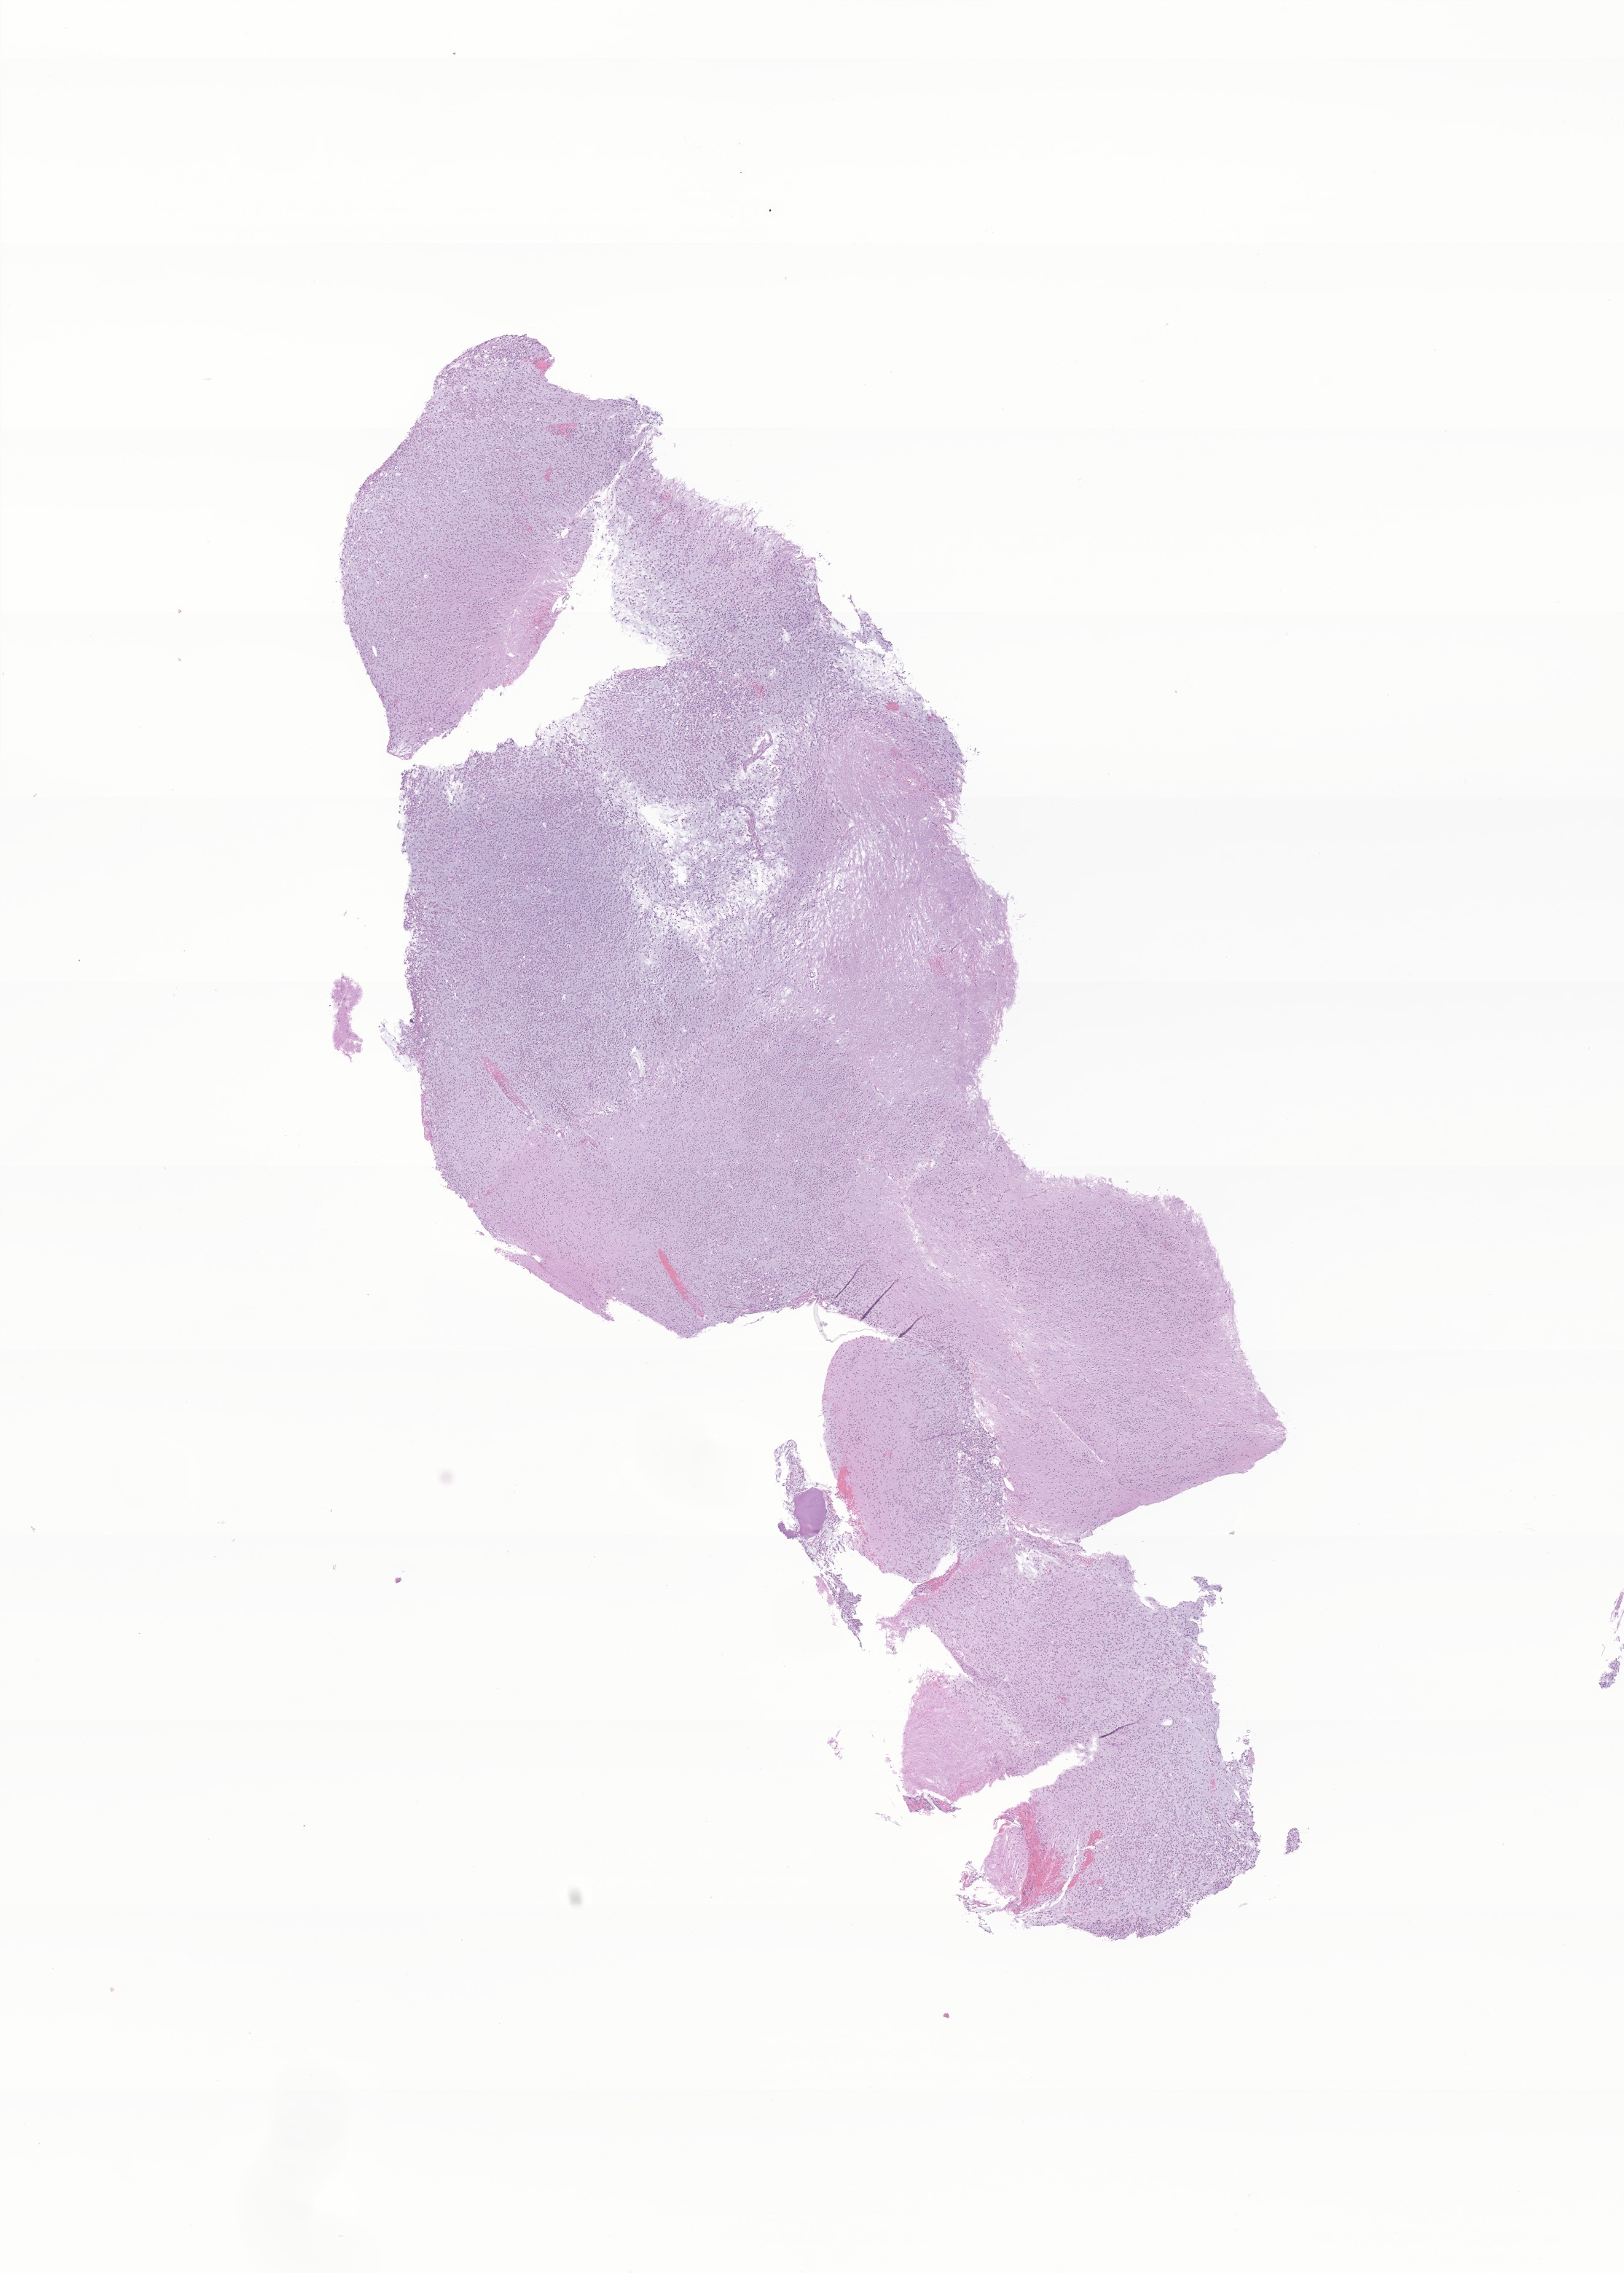
Digitized hematoxylin and eosin (H&E)-stained section of tumor tissue from the occipital lobe — low-resolution overview of the scanned area, about 9.4 x 13.1 mm; FFPE section. Patient female; age 211 months (17 years 7 months).
Recorded diagnosis: Neuroepithelioma, NOS.